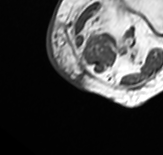
MRI of an extremity soft-tissue mass, one axial slice. Position 2 of 65 along the scan axis. MR volume resampled by the dataset authors to the PET/CT grid (not the native acquisition matrix). 163 × 155 image matrix. Female patient. Case-level facts recorded for this patient, not image findings: histological type: pleomorphic leiomyosarcoma; grade: high; site of the primary tumour: left thigh.
Outlined on this slice (expert contour drawn on MRI and transferred to this co-registered scan by the dataset authors):
- gross tumour volume including surrounding oedema: bounding box [x1, y1, x2, y2] px = [71, 0, 141, 68]